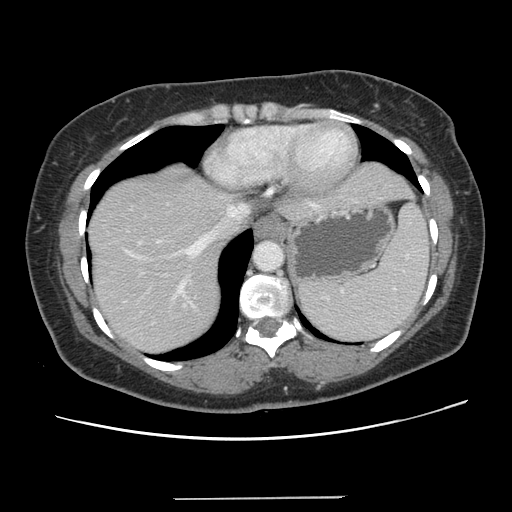
Contrast-enhanced abdominal CT, one axial slice. 120 kVp. Intravenous contrast given. Soft-tissue window (W 400 / L 40 HU). 2.5 mm slice thickness. 512 × 512 image matrix, field of view 366 × 366 mm. Female patient, age 53 years. Case-level facts recorded for this patient, not image findings: diagnosis: colorectal cancer liver metastases, imaged before liver resection; multiple liver metastases: no; largest metastasis: 14.5 cm.
Outlined on this slice (outlined manually by an expert reader):
- hepatic veins: bounding box <113,197,316,292> (left, top, right, bottom; pixels)
- liver: <88,162,410,354>
- planned liver remnant (the part of the liver to remain after resection): <88,209,245,354>
- portal vein (with intrahepatic branches): <137,239,196,310>